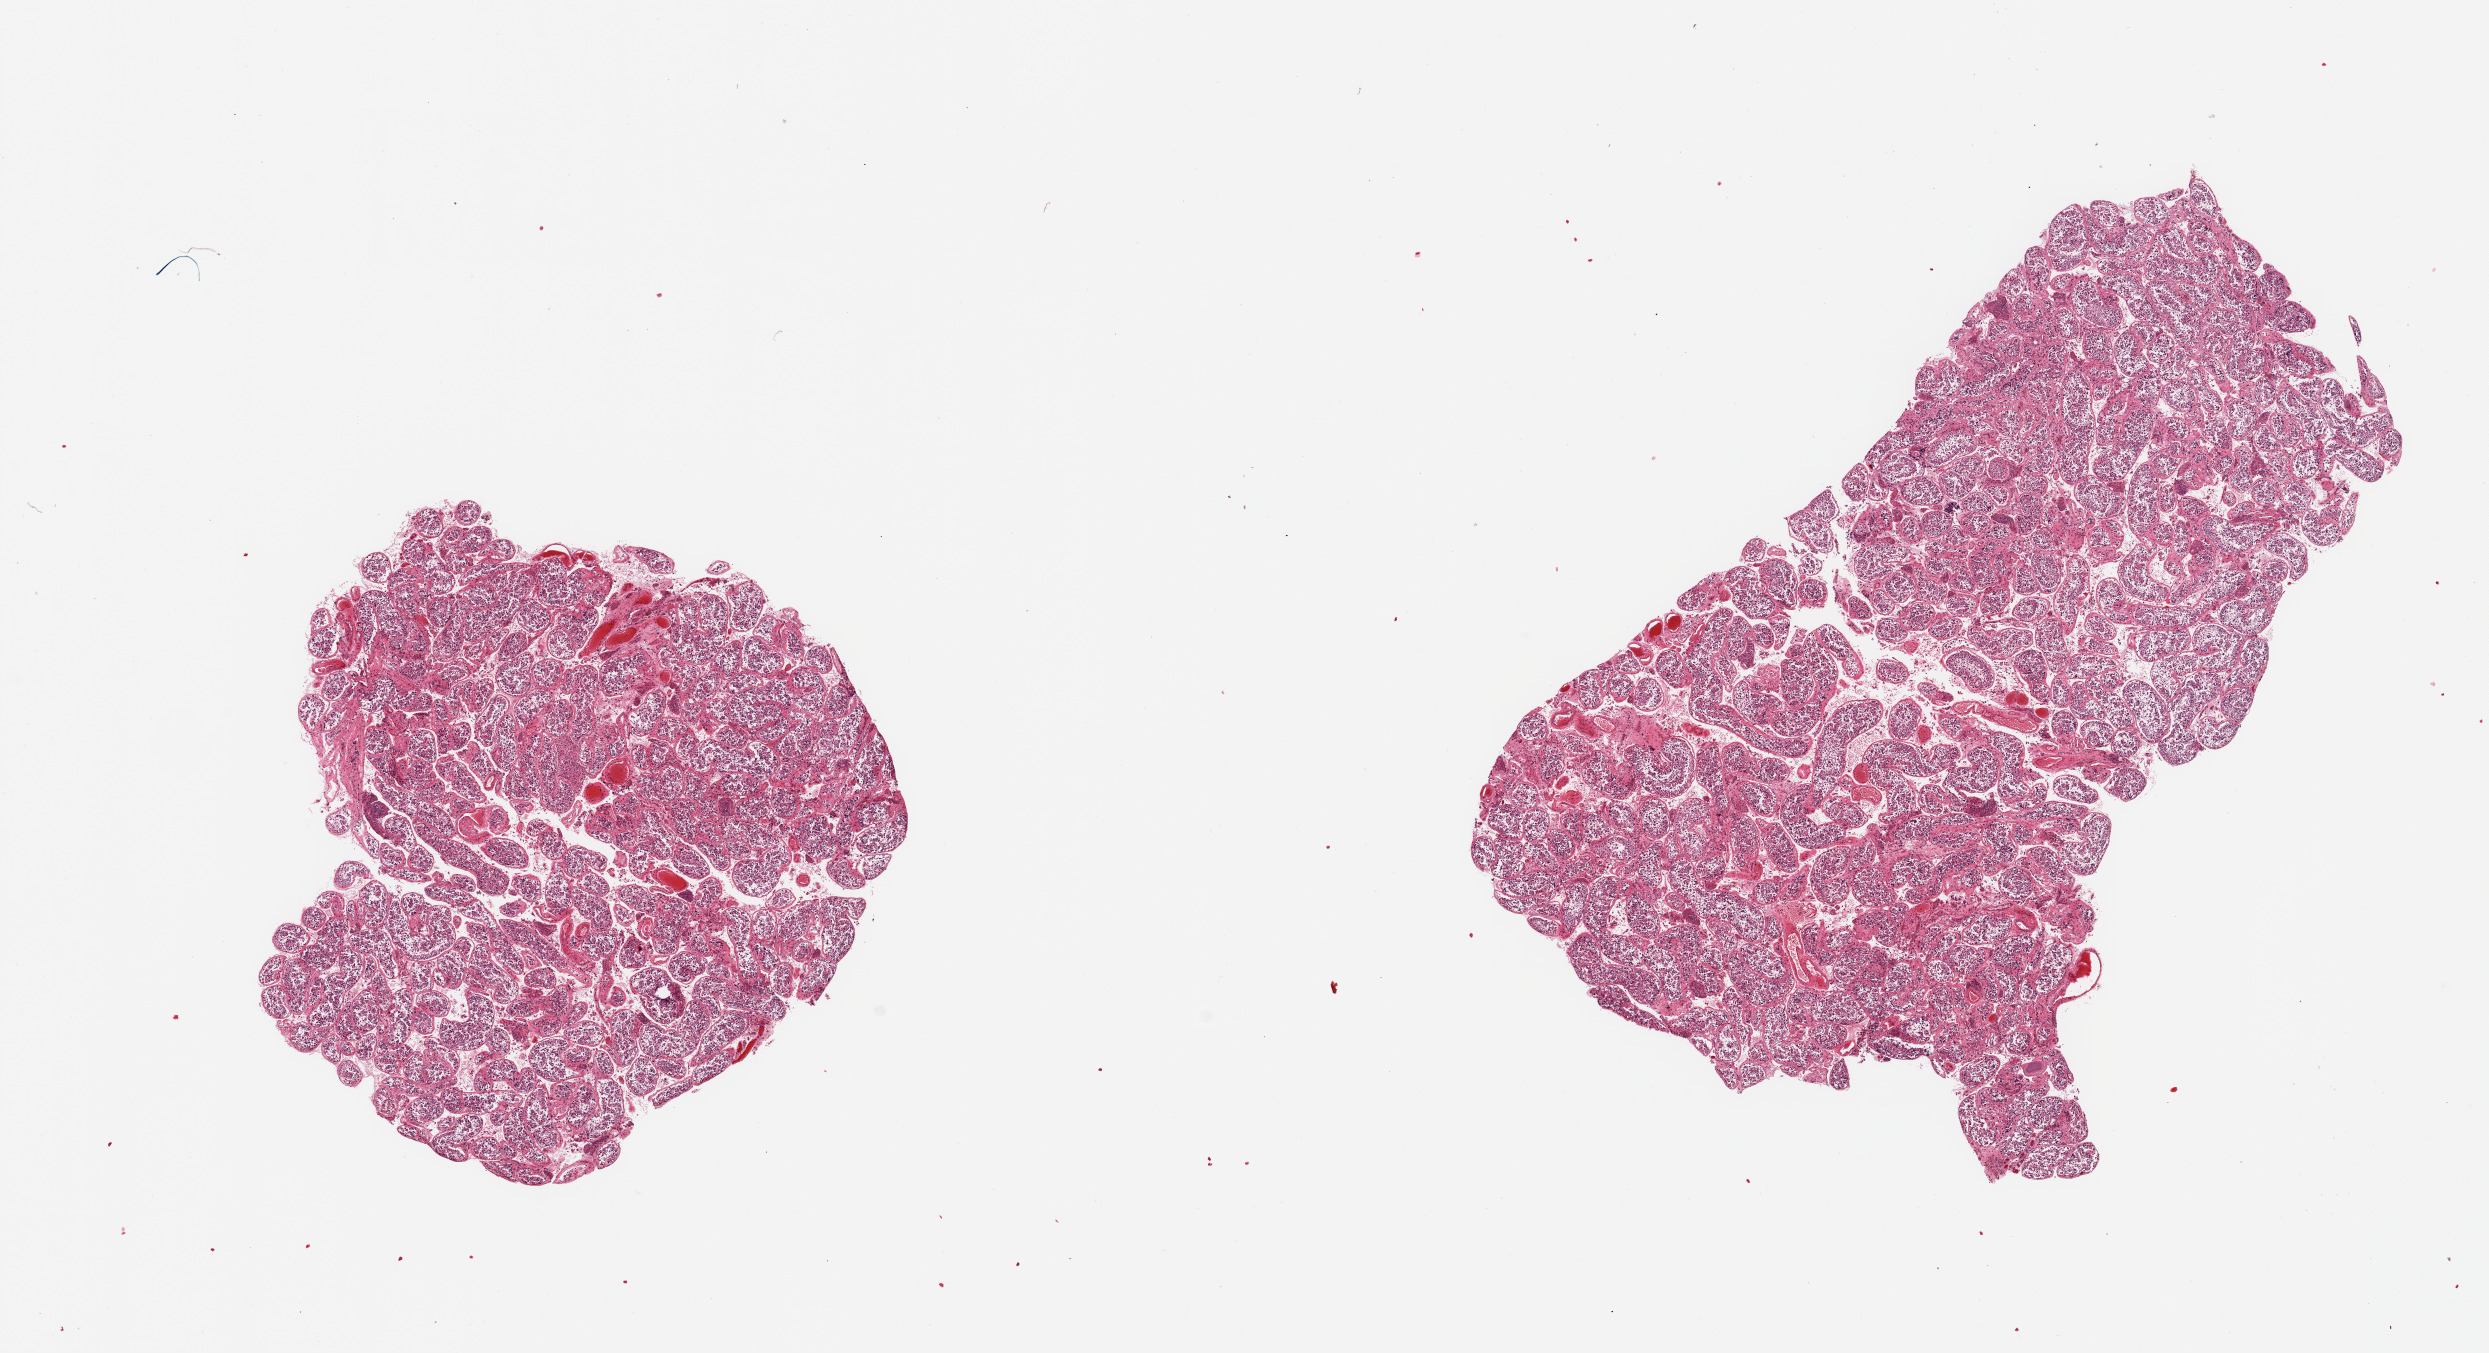
Hematoxylin and eosin (H&E) whole-slide image, shown as a low-resolution overview of the whole scanned area (about 19.7 x 10.7 mm), PAXgene-fixed, paraffin-embedded tissue, section of testis (target tissue), tissue donor sample. Donor: male.
Review note (as recorded): 2 pieces; spermatogenesis present but decreased; congestion.